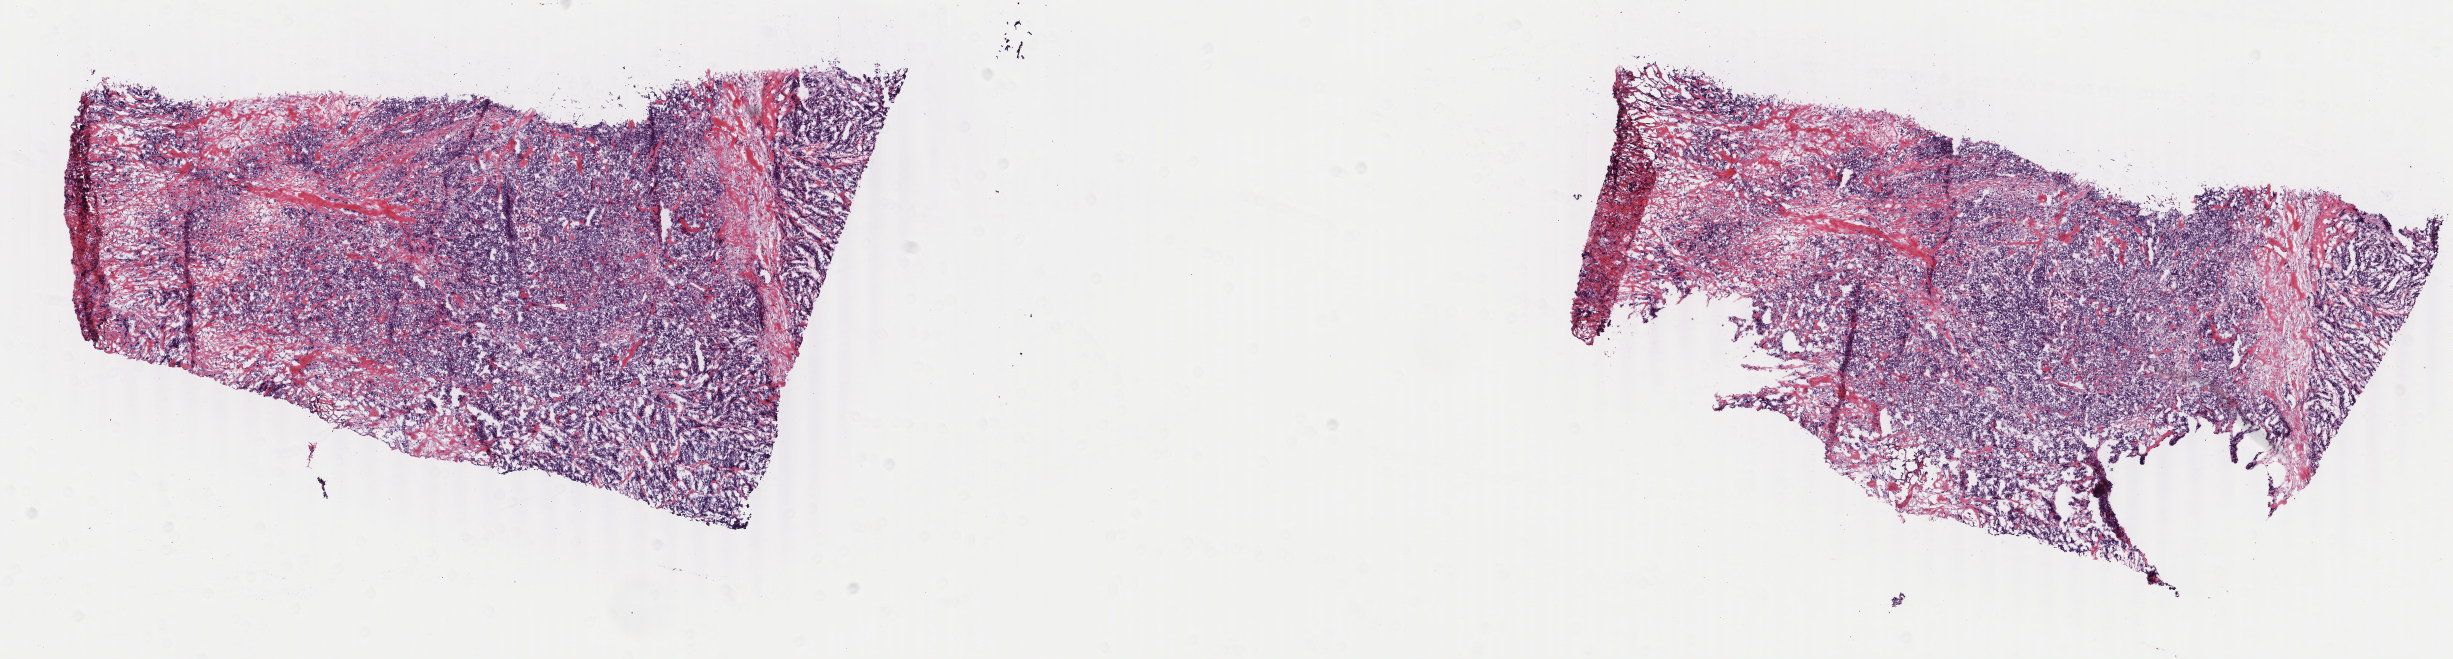
Whole-slide histology image, Hematoxylin and eosin (H&E) stained — shown as a low-resolution overview of the whole scanned area (about 19.5 x 5.2 mm, slide scanned at 40x). Frozen section. Primary tumour sample from the breast. Patient: female, age at initial diagnosis 76 years. Composition of this section per pathologist review: tumour cells 90%, tumour nuclei 90%, normal cells 0%, stromal cells 10%, necrosis 0%. Inflammatory infiltration, as recorded: lymphocyte infiltration 1%, monocyte infiltration 0%, neutrophil infiltration 0%.
AJCC pathologic stage: IIA (6th edition). Histologic diagnosis: Infiltrating duct carcinoma, NOS.